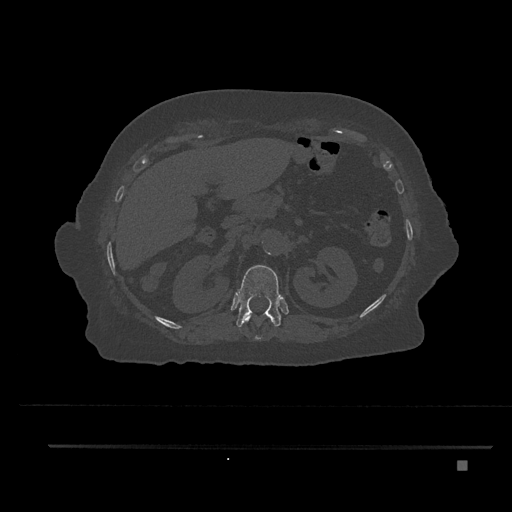
CT including the spine, one axial slice. Slice 274 of 797 in the series (ordered by position). Bone window (W 1800 / L 400 HU). 0.5 mm slice thickness. 512 × 512 image matrix, field of view 437 × 437 mm. Female patient, age 76 years. Case-level facts recorded for this patient, not image findings: primary cancer: lung.
Structures marked on this image (semi-automatically segmented with operator editing):
- T11 vertebra: bounding box (x1, y1, x2, y2) in pixels: (243, 313, 273, 340)
- T12 vertebra: (236, 265, 283, 328)